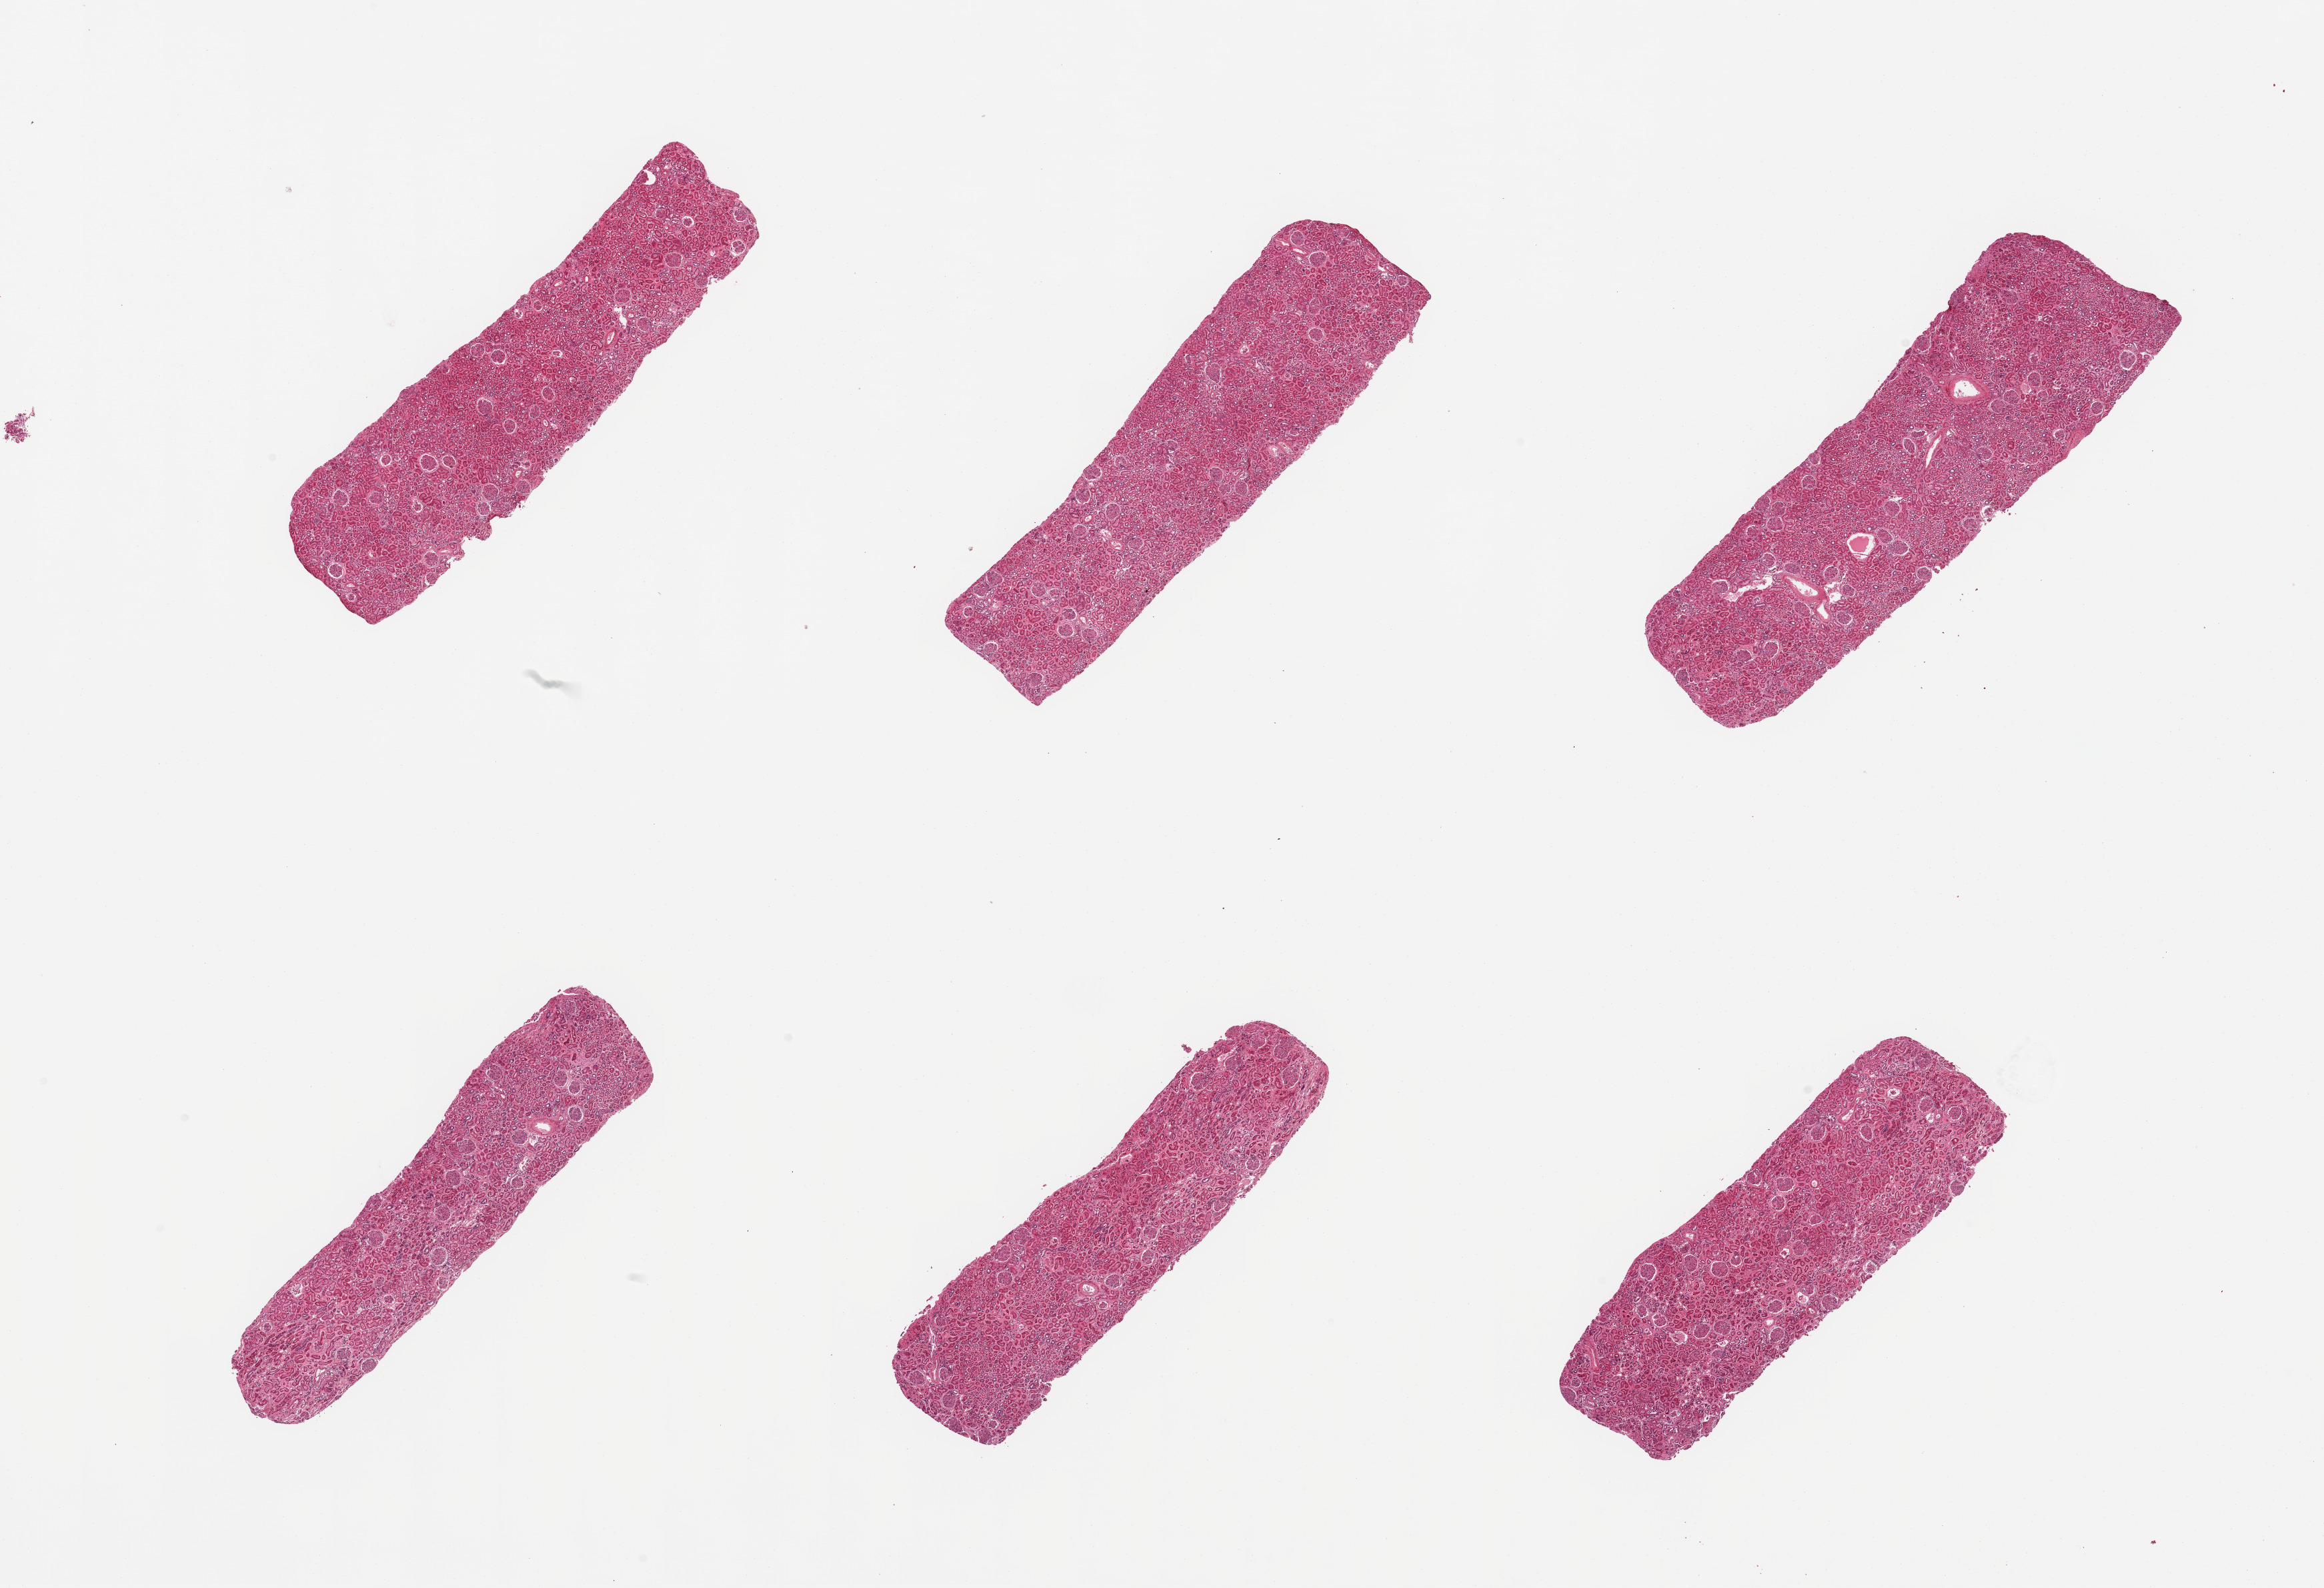
Hematoxylin and eosin (H&E) whole-slide image — low-resolution overview of the scanned area, about 27.6 x 18.8 mm (acquisition: 20x scan), PAXgene-fixed, paraffin-embedded tissue, section of renal cortex (target tissue), donor tissue sample. Donor: male.
Reviewer comment on this tissue sample: 6 pieces; no sign of chronic disease; tubules in varying state of preservation.